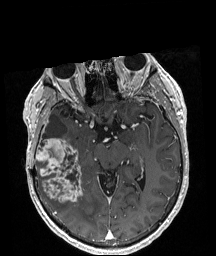
Brain MRI from a brain-tumour surgery series, one axial slice. Slice 118 of 208 in the series (ordered by position). T1-weighted post-contrast. 1 mm slice thickness. 216 × 256 image matrix. Case-level facts recorded for this patient, not image findings: histopathology: Astrocytoma; WHO grade: 4; IDH mutation: yes.
Structures marked on this image (outlined manually by an expert reader):
- tumour: bounding box (x1, y1, x2, y2) in pixels: (36, 136, 82, 202)